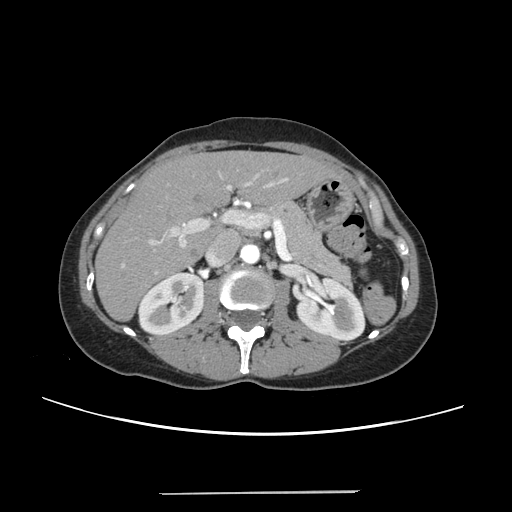
Contrast-enhanced abdominal CT, one axial slice; position 131 of 240 along the scan axis; intravenous contrast given; soft-tissue window (W 400 / L 40 HU); 1.25 mm slice thickness; 512 × 512 image matrix. Female patient, age 60 years. Case-level facts recorded for this patient, not image findings: diagnosis: colorectal cancer liver metastases, imaged before liver resection; multiple liver metastases: no; largest metastasis: 1.5 cm; disease in both lobes: no.
Annotated regions visible in this slice (manually delineated by an expert):
- liver: bounding box <97,152,335,319> (left, top, right, bottom; pixels)
- planned liver remnant (the part of the liver to remain after resection): <97,152,333,320>
- portal vein (with intrahepatic branches): <122,175,289,274>